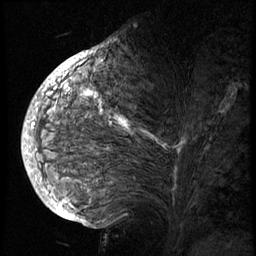
Breast MRI (dynamic contrast-enhanced), one sagittal slice. Position 36 of 74 along the scan axis. 3 images stored at this slice position (order not interpretable as contrast timing). 1.5 T. TE 4.2 ms, TR 8.9 ms. 2.5 mm slice thickness. 256 × 256 image matrix, field of view 200 × 200 mm. Female patient, age 57 years. From the clinical record (not read from this slice): setting: breast cancer imaged before/during neoadjuvant chemotherapy; receptor status: HER2-positive.
Annotated regions visible in this slice (semi-automatic segmentation, software-assisted and operator-edited):
- analysis volume of interest (the breast-tissue region the enhancement analysis was run in; not a lesion): bounding box [x1, y1, x2, y2] px = [40, 62, 233, 175]
- tumour enhancement mask (voxels above the 140 % enhancement threshold inside the analysis volume of interest): [40, 62, 187, 172]